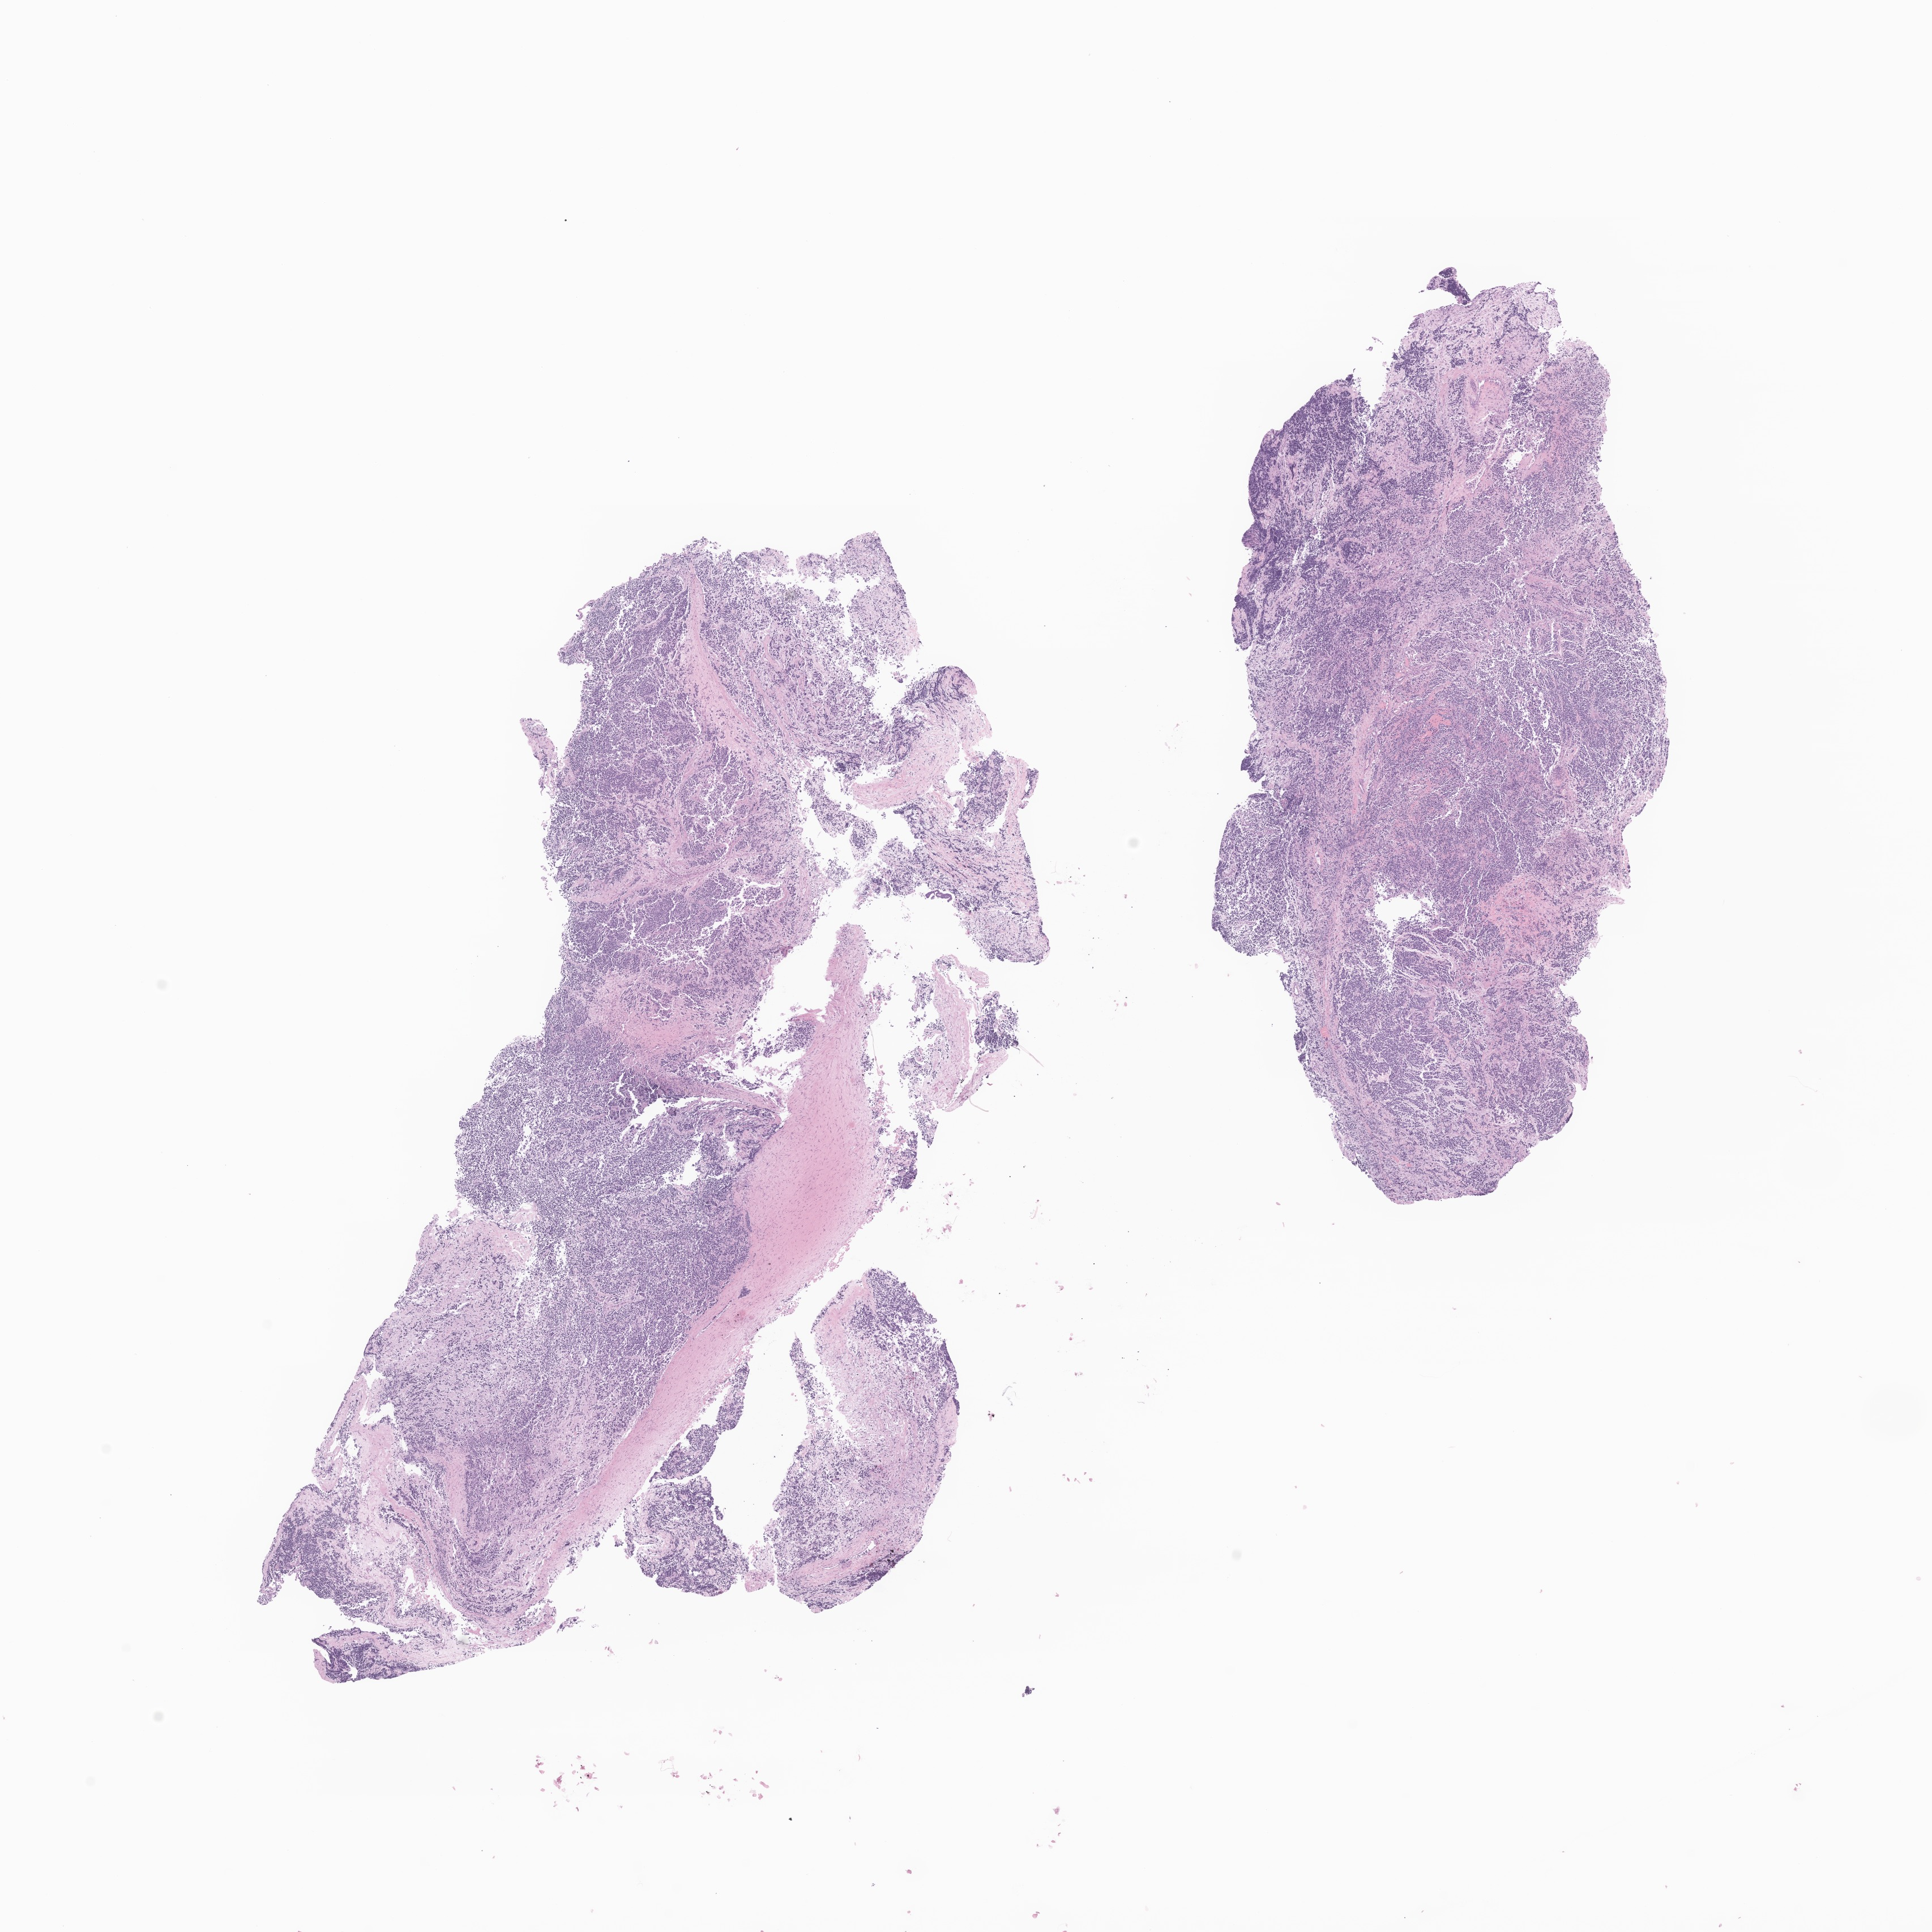
Hematoxylin and eosin (H&E) whole-slide image of tumor tissue from the adrenal gland — whole scanned area (about 14.4 x 14.4 mm) shown as a low-resolution overview; formalin-fixed, paraffin-embedded (FFPE) tissue. Patient female; age 567 days (about 1.6 years).
Recorded diagnosis: Neuroblastoma, NOS.